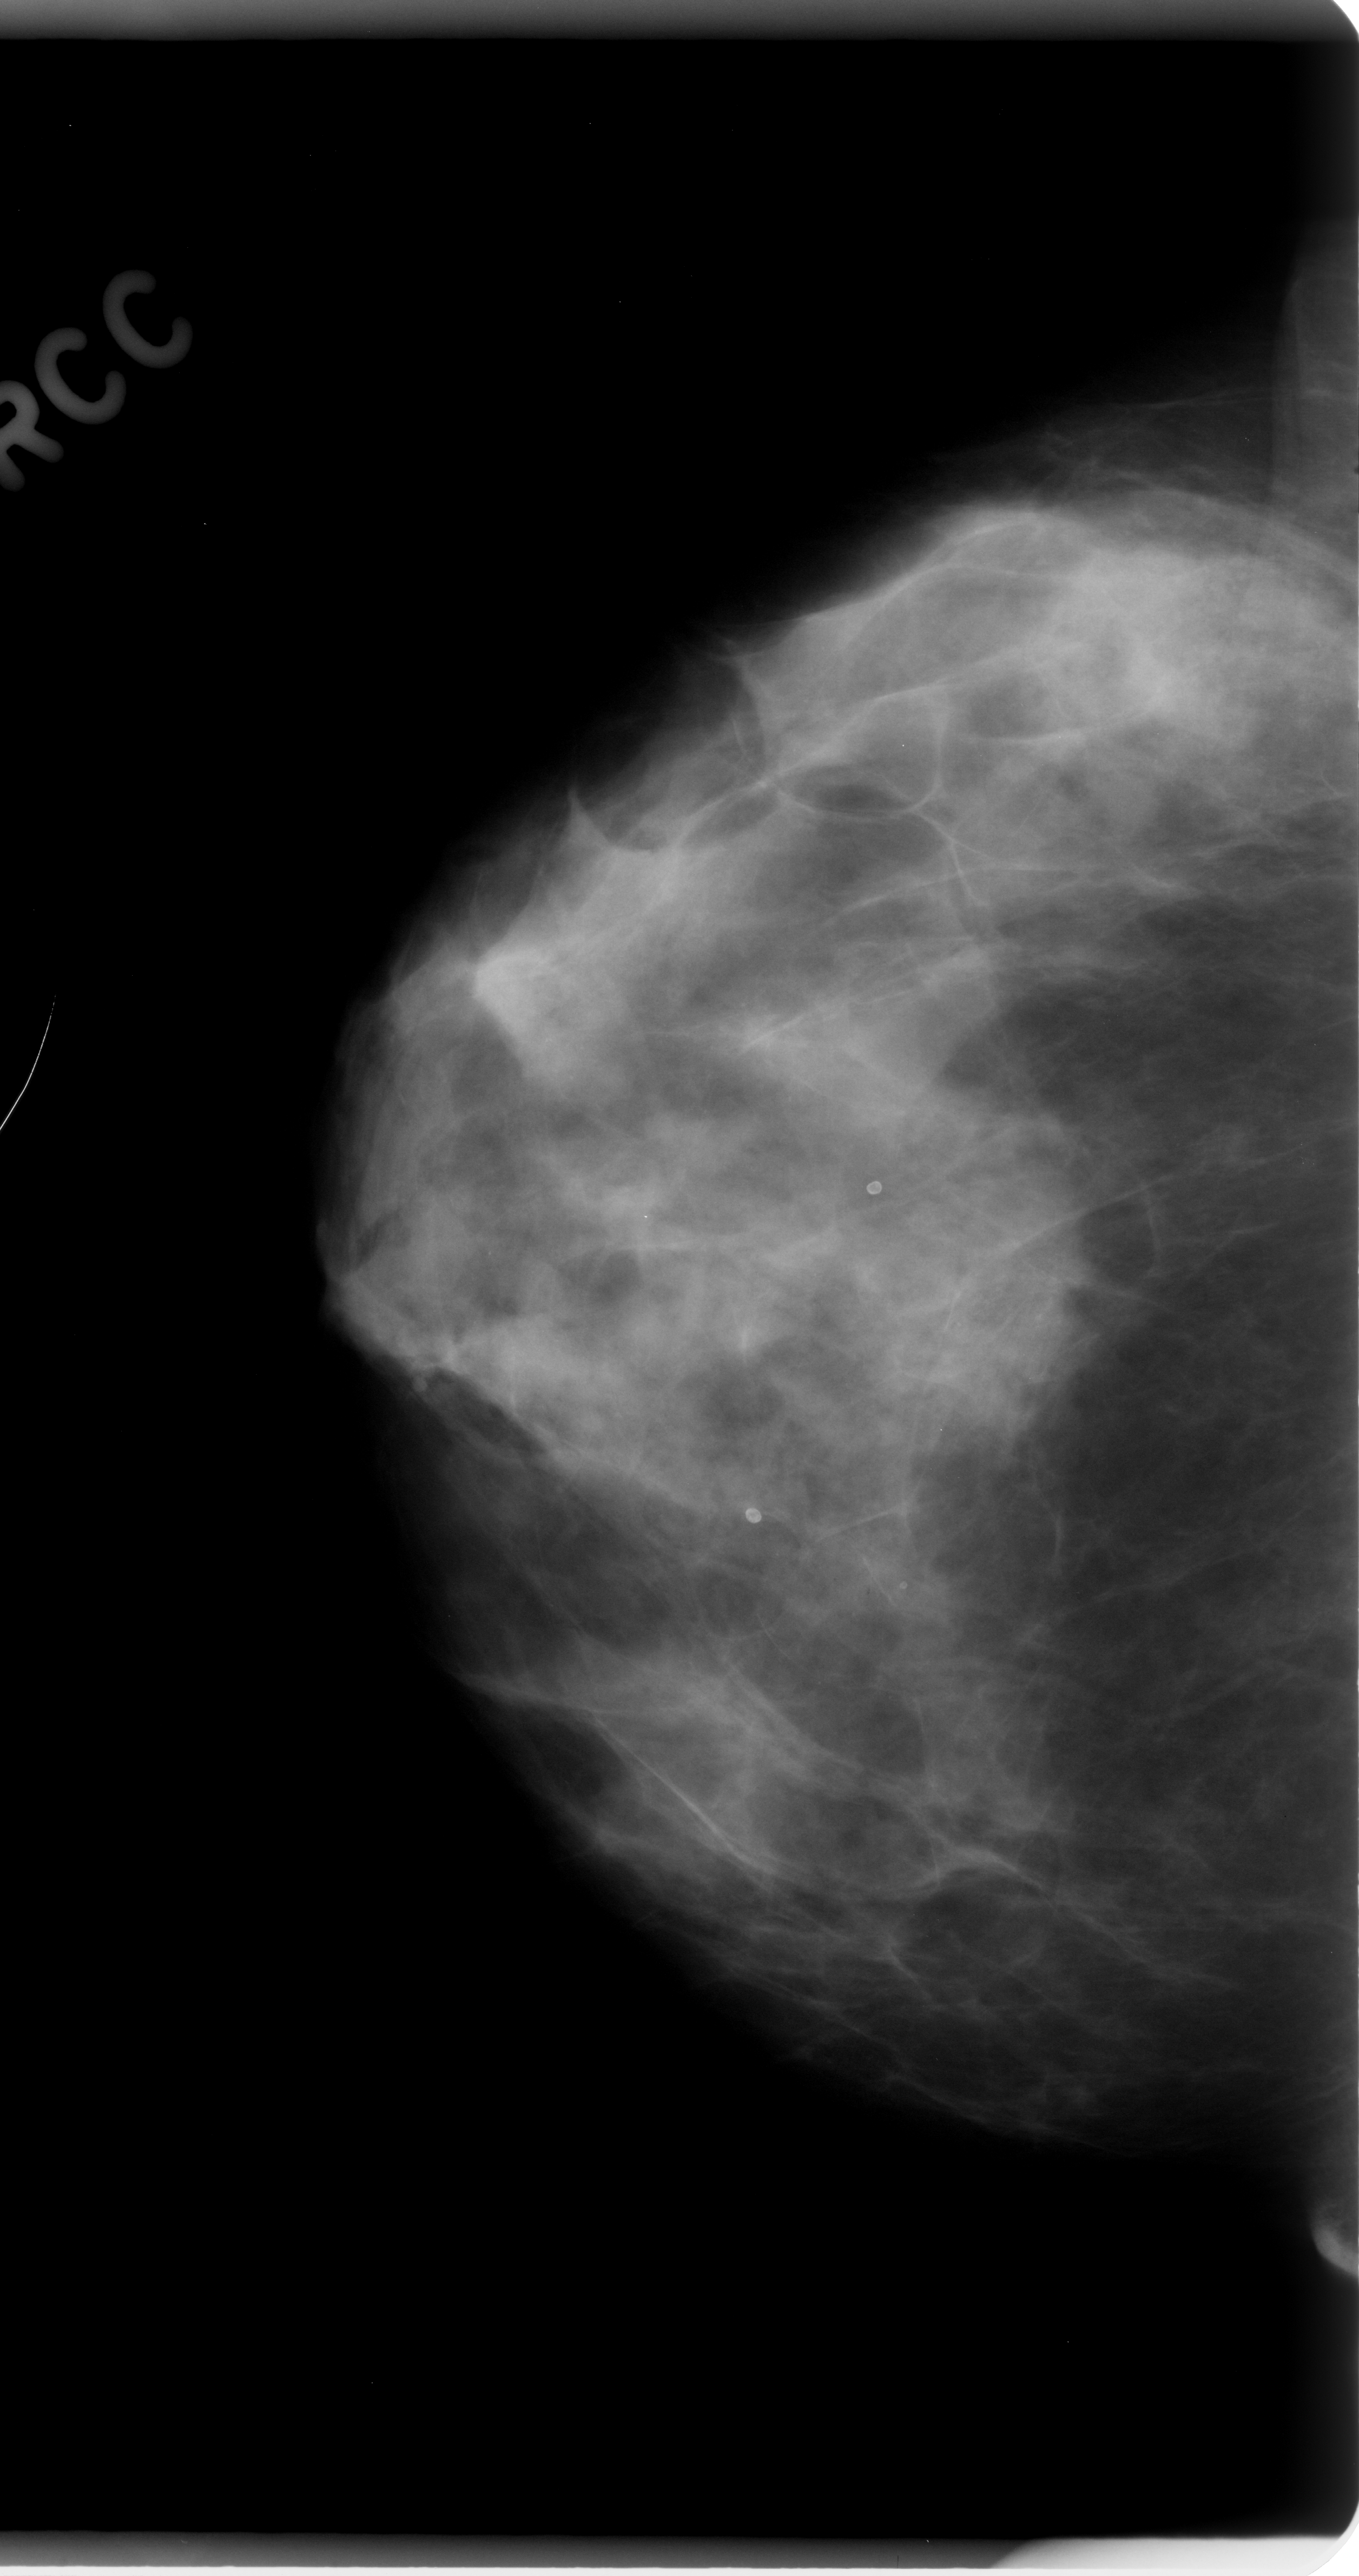
Digitized screen-film mammogram, right breast, craniocaudal (CC) view, BI-RADS breast density category 3 (scale 1–4).
Abnormality record for this image: calcifications, morphology amorphous, distribution clustered; BI-RADS assessment category 5; subtlety rating 5 on a 1 (subtle) to 5 (obvious) scale; pathology result (as recorded, not read from the image): malignant.